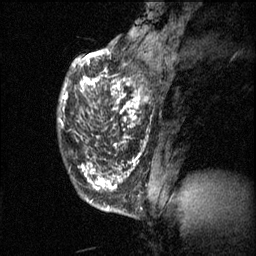
Breast MRI (dynamic contrast-enhanced), one sagittal slice; slice 15 of 60 in the series (ordered by position); 3 images stored at this slice position (order not interpretable as contrast timing); 1.5 T; TE 4.2 ms, TR 11.1 ms; 2 mm slice thickness; 256 × 256 image matrix. Patient: female, 50 years.
Structures marked on this image (semi-automatically segmented with operator editing):
- analysis volume of interest (the breast-tissue region the enhancement analysis was run in; not a lesion): box from (x=81, y=68) to (x=153, y=141) px
- tumour enhancement mask (voxels above the 70 % enhancement threshold inside the analysis volume of interest): (x=81, y=68)–(x=145, y=141)